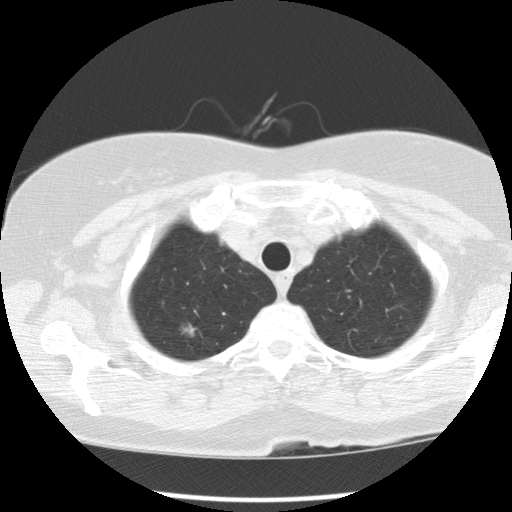
Low-dose screening chest CT, one axial slice; slice 109 of 122 in the series (ordered by position); 120 kVp; lung window (W 1500 / L -600 HU); 512 × 512 image matrix.
Structures marked on this image (manually delineated by an expert):
- lesion 1 (tumor, upper lobe of right lung): bounding box [x1, y1, x2, y2] px = [181, 320, 197, 337]